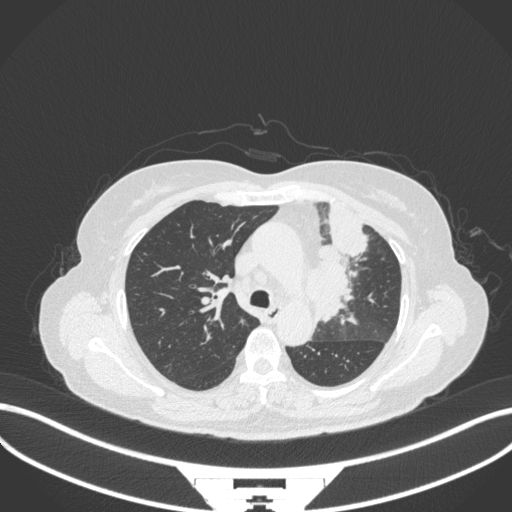
Chest CT, one axial slice. Slice 229 of 382 in the series (ordered by position). Lung window (W 1500 / L -600 HU). 1 mm slice thickness. 512 × 512 image matrix, field of view 400 × 400 mm. Female patient, age 64 years. Case-level facts recorded for this patient, not image findings: clinical TNM (as recorded): T2a N2 M0.
Annotated regions visible in this slice (bounding box drawn by a radiologist):
- lung tumour (recorded histology: adenocarcinoma): bounding box [x1, y1, x2, y2] px = [306, 199, 375, 325]